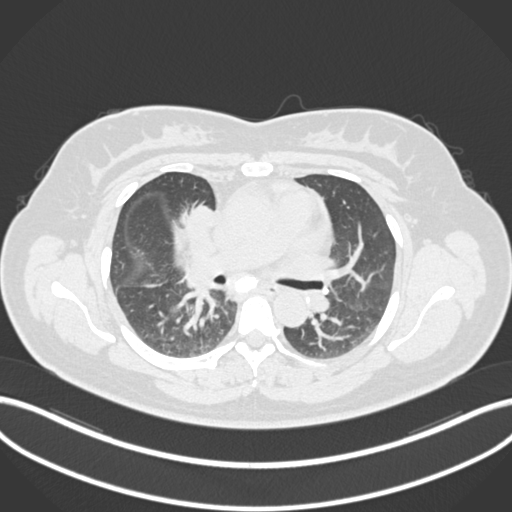
Chest CT, one axial slice; slice 100 of 183 in the series (ordered by position); 120 kVp; lung window (W 1500 / L -600 HU); 512 × 512 image matrix, field of view 400 × 400 mm. Patient: female, 46 years. From the clinical record (not read from this slice): clinical TNM (as recorded): T2a N1 M0.
Outlined on this slice (rectangle marked by the reading radiologist):
- lung tumour (recorded histology: adenocarcinoma): bounding box <180,202,216,231> (left, top, right, bottom; pixels)